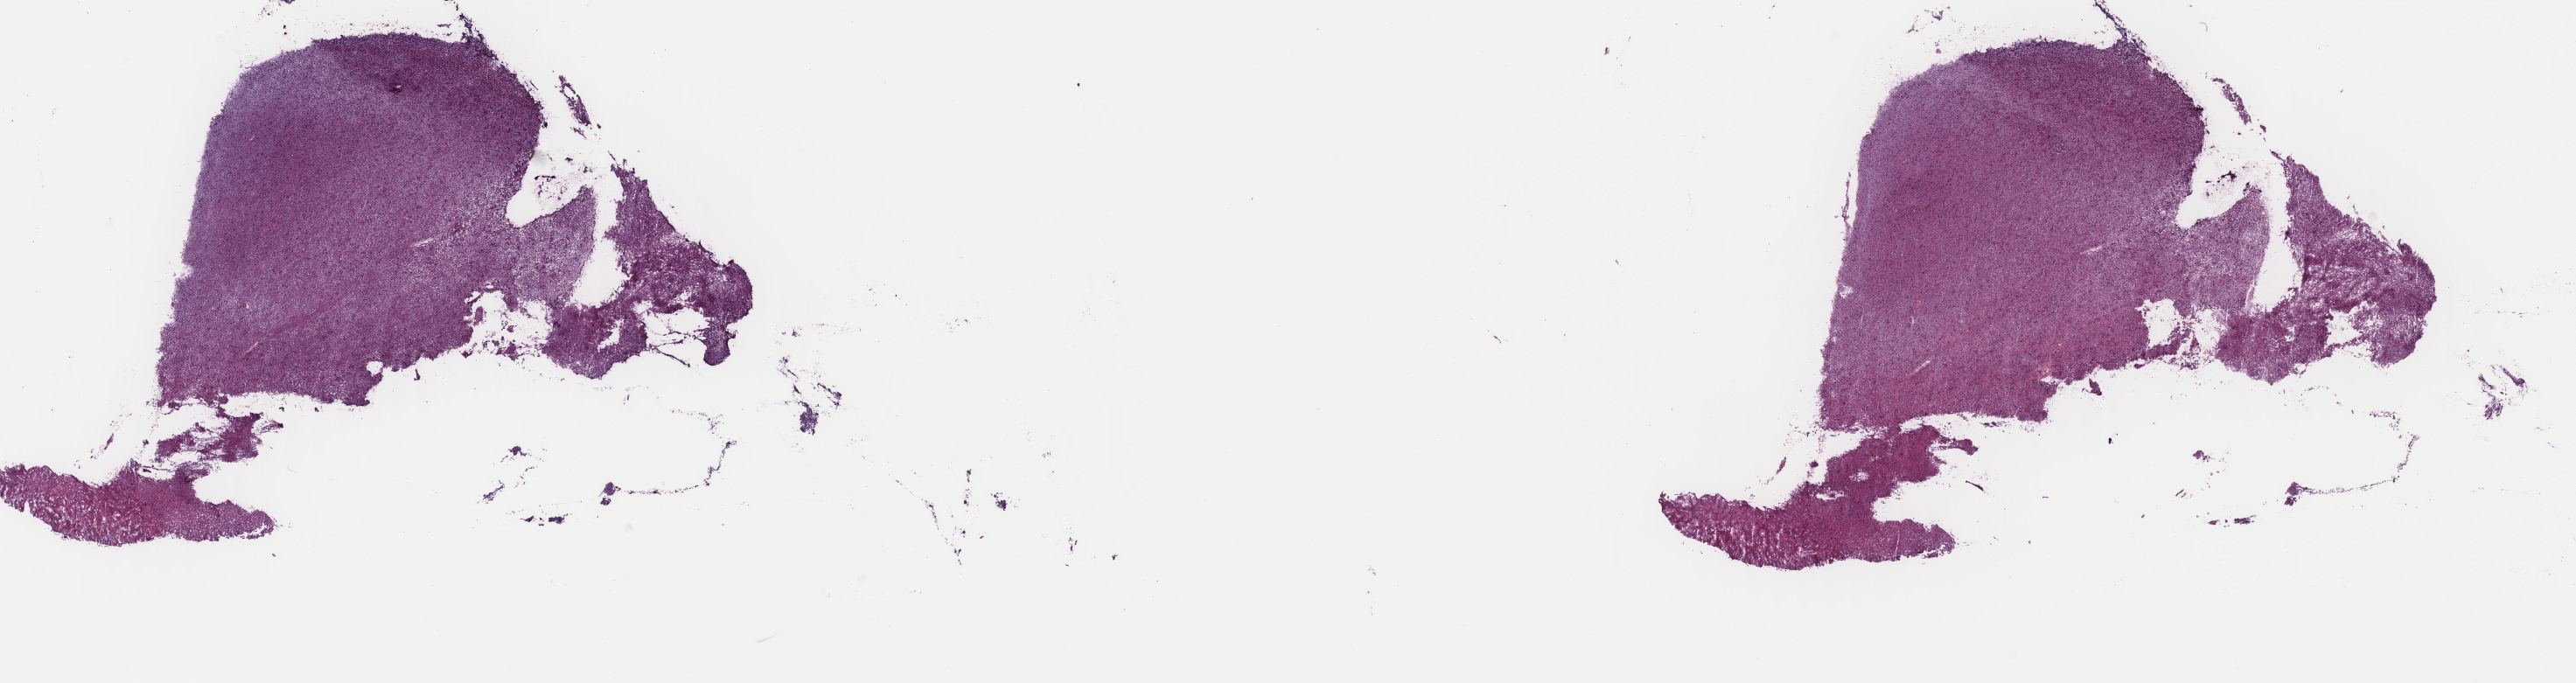
Whole-slide histology image, H&E — shown as a low-resolution overview of the whole scanned area (about 23.4 x 6.2 mm). Frozen section from the top of the tissue portion. Sample: primary tumour, brain. Male, age 48 years at initial diagnosis. Histologic grade: G3 (poorly differentiated). Slide review estimates, as recorded: tumour cells 40%, tumour nuclei 80%, normal cells 10%, stromal cells 50%, necrosis 0%. Inflammatory infiltration, as recorded: lymphocyte infiltration 0%, monocyte infiltration 0%, neutrophil infiltration 0%.
Histologic diagnosis: Astrocytoma, anaplastic (cerebrum).